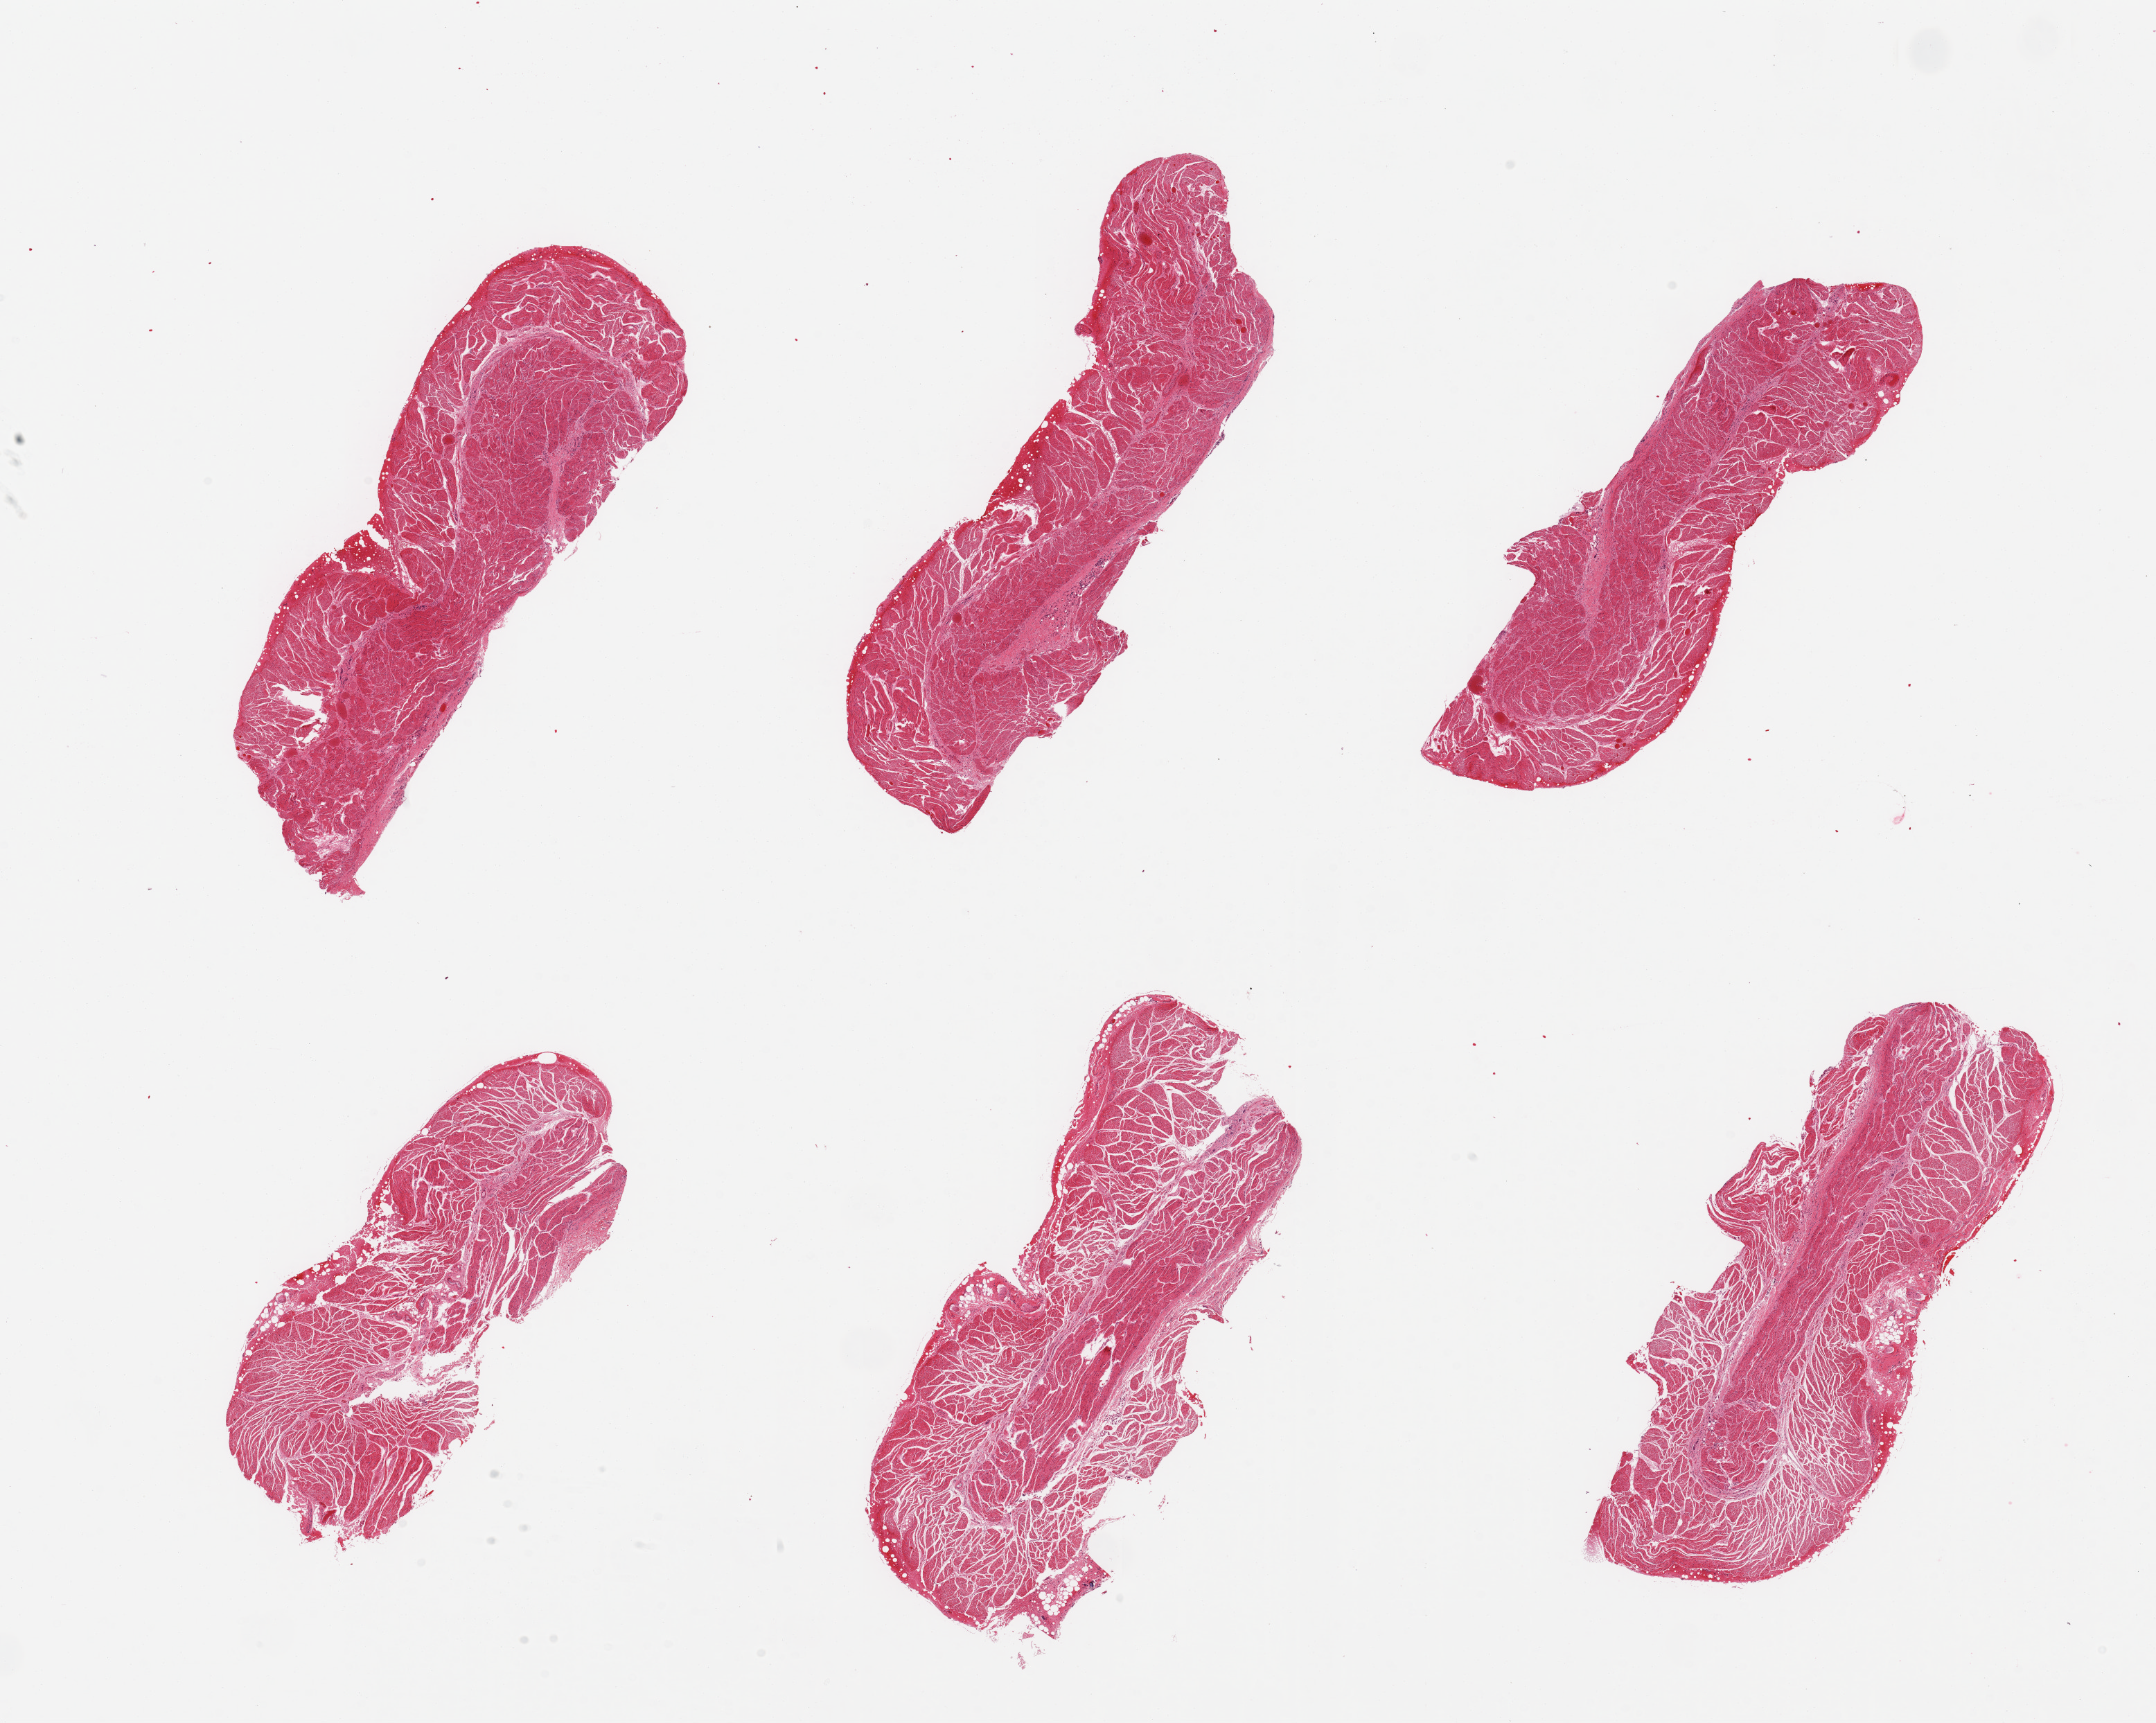
Digitized hematoxylin and eosin (H&E)-stained section — low-resolution overview of the scanned area, about 24.6 x 19.7 mm; PAXgene-fixed, paraffin-embedded tissue; target tissue: esophageal muscle; tissue donor sample. Male donor.
Review note (as recorded): 6 pieces, confirmed target muscularis.